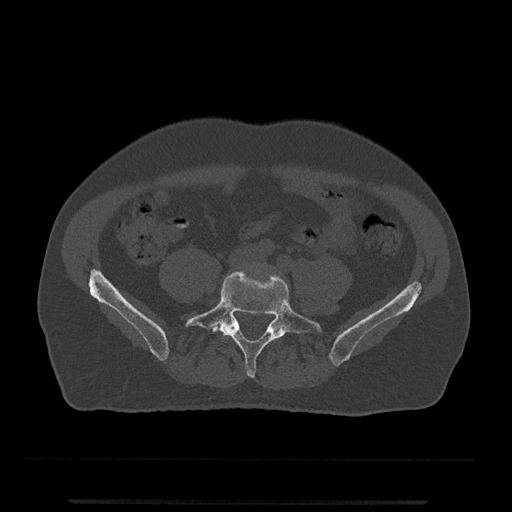
CT including the spine, one axial slice. Bone window (W 1800 / L 400 HU). 0.5 mm slice thickness. 512 × 512 image matrix. Patient: male, 63 years. From the clinical record (not read from this slice): primary cancer: prostate.
Annotated regions visible in this slice (semi-automatically segmented with operator editing):
- L4 vertebra: bounding box (x1, y1, x2, y2) in pixels: (231, 320, 235, 327)
- L5 vertebra: (185, 270, 322, 378)